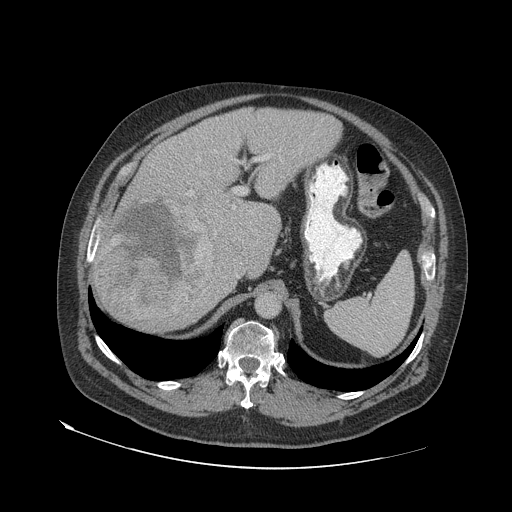
Contrast-enhanced abdominal CT (liver protocol), one axial slice. Slice 45 of 79 in the series (ordered by position). Soft-tissue window (W 400 / L 40 HU). 2.5 mm slice thickness. 512 × 512 image matrix. Case-level facts recorded for this patient, not image findings: diagnosis: hepatocellular carcinoma (patient treated with transarterial chemoembolisation; whether this scan precedes or follows treatment is not stated here); TNM stage (as recorded): Stage-IVA; Child-Pugh class: A; tumour differentiation: well differentiated; tumour nodularity: multinodular.
Outlined on this slice (semi-automatically segmented with operator editing):
- liver parenchyma outside the tumour (the mass and vessels are separate outlines, so this box may not span the whole liver): bounding box <92,108,342,330> (left, top, right, bottom; pixels)
- mass: <99,196,216,320>
- liver vessels: <95,155,270,246>